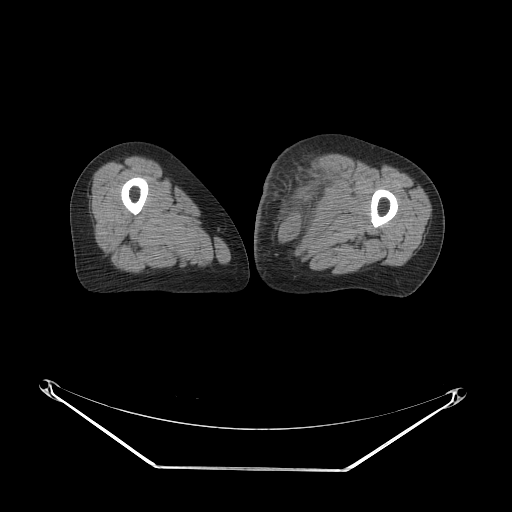
CT of an extremity soft-tissue mass (from a PET/CT study), one axial slice. Slice 43 of 91 in the series (ordered by position). Reconstruction kernel STANDARD. 140 kVp. Soft-tissue window (W 400 / L 40 HU). 3.75 mm slice thickness. 512 × 512 image matrix, field of view 500 × 500 mm. Female patient. From the clinical record (not read from this slice): histological type: pleomorphic leiomyosarcoma; grade: high; site of the primary tumour: left thigh.
Structures marked on this image (expert contour drawn on MRI and transferred to this co-registered scan by the dataset authors):
- gross tumour volume including surrounding oedema: bounding box [x1, y1, x2, y2] px = [263, 155, 344, 238]
- gross tumour volume (mass): [283, 155, 332, 220]